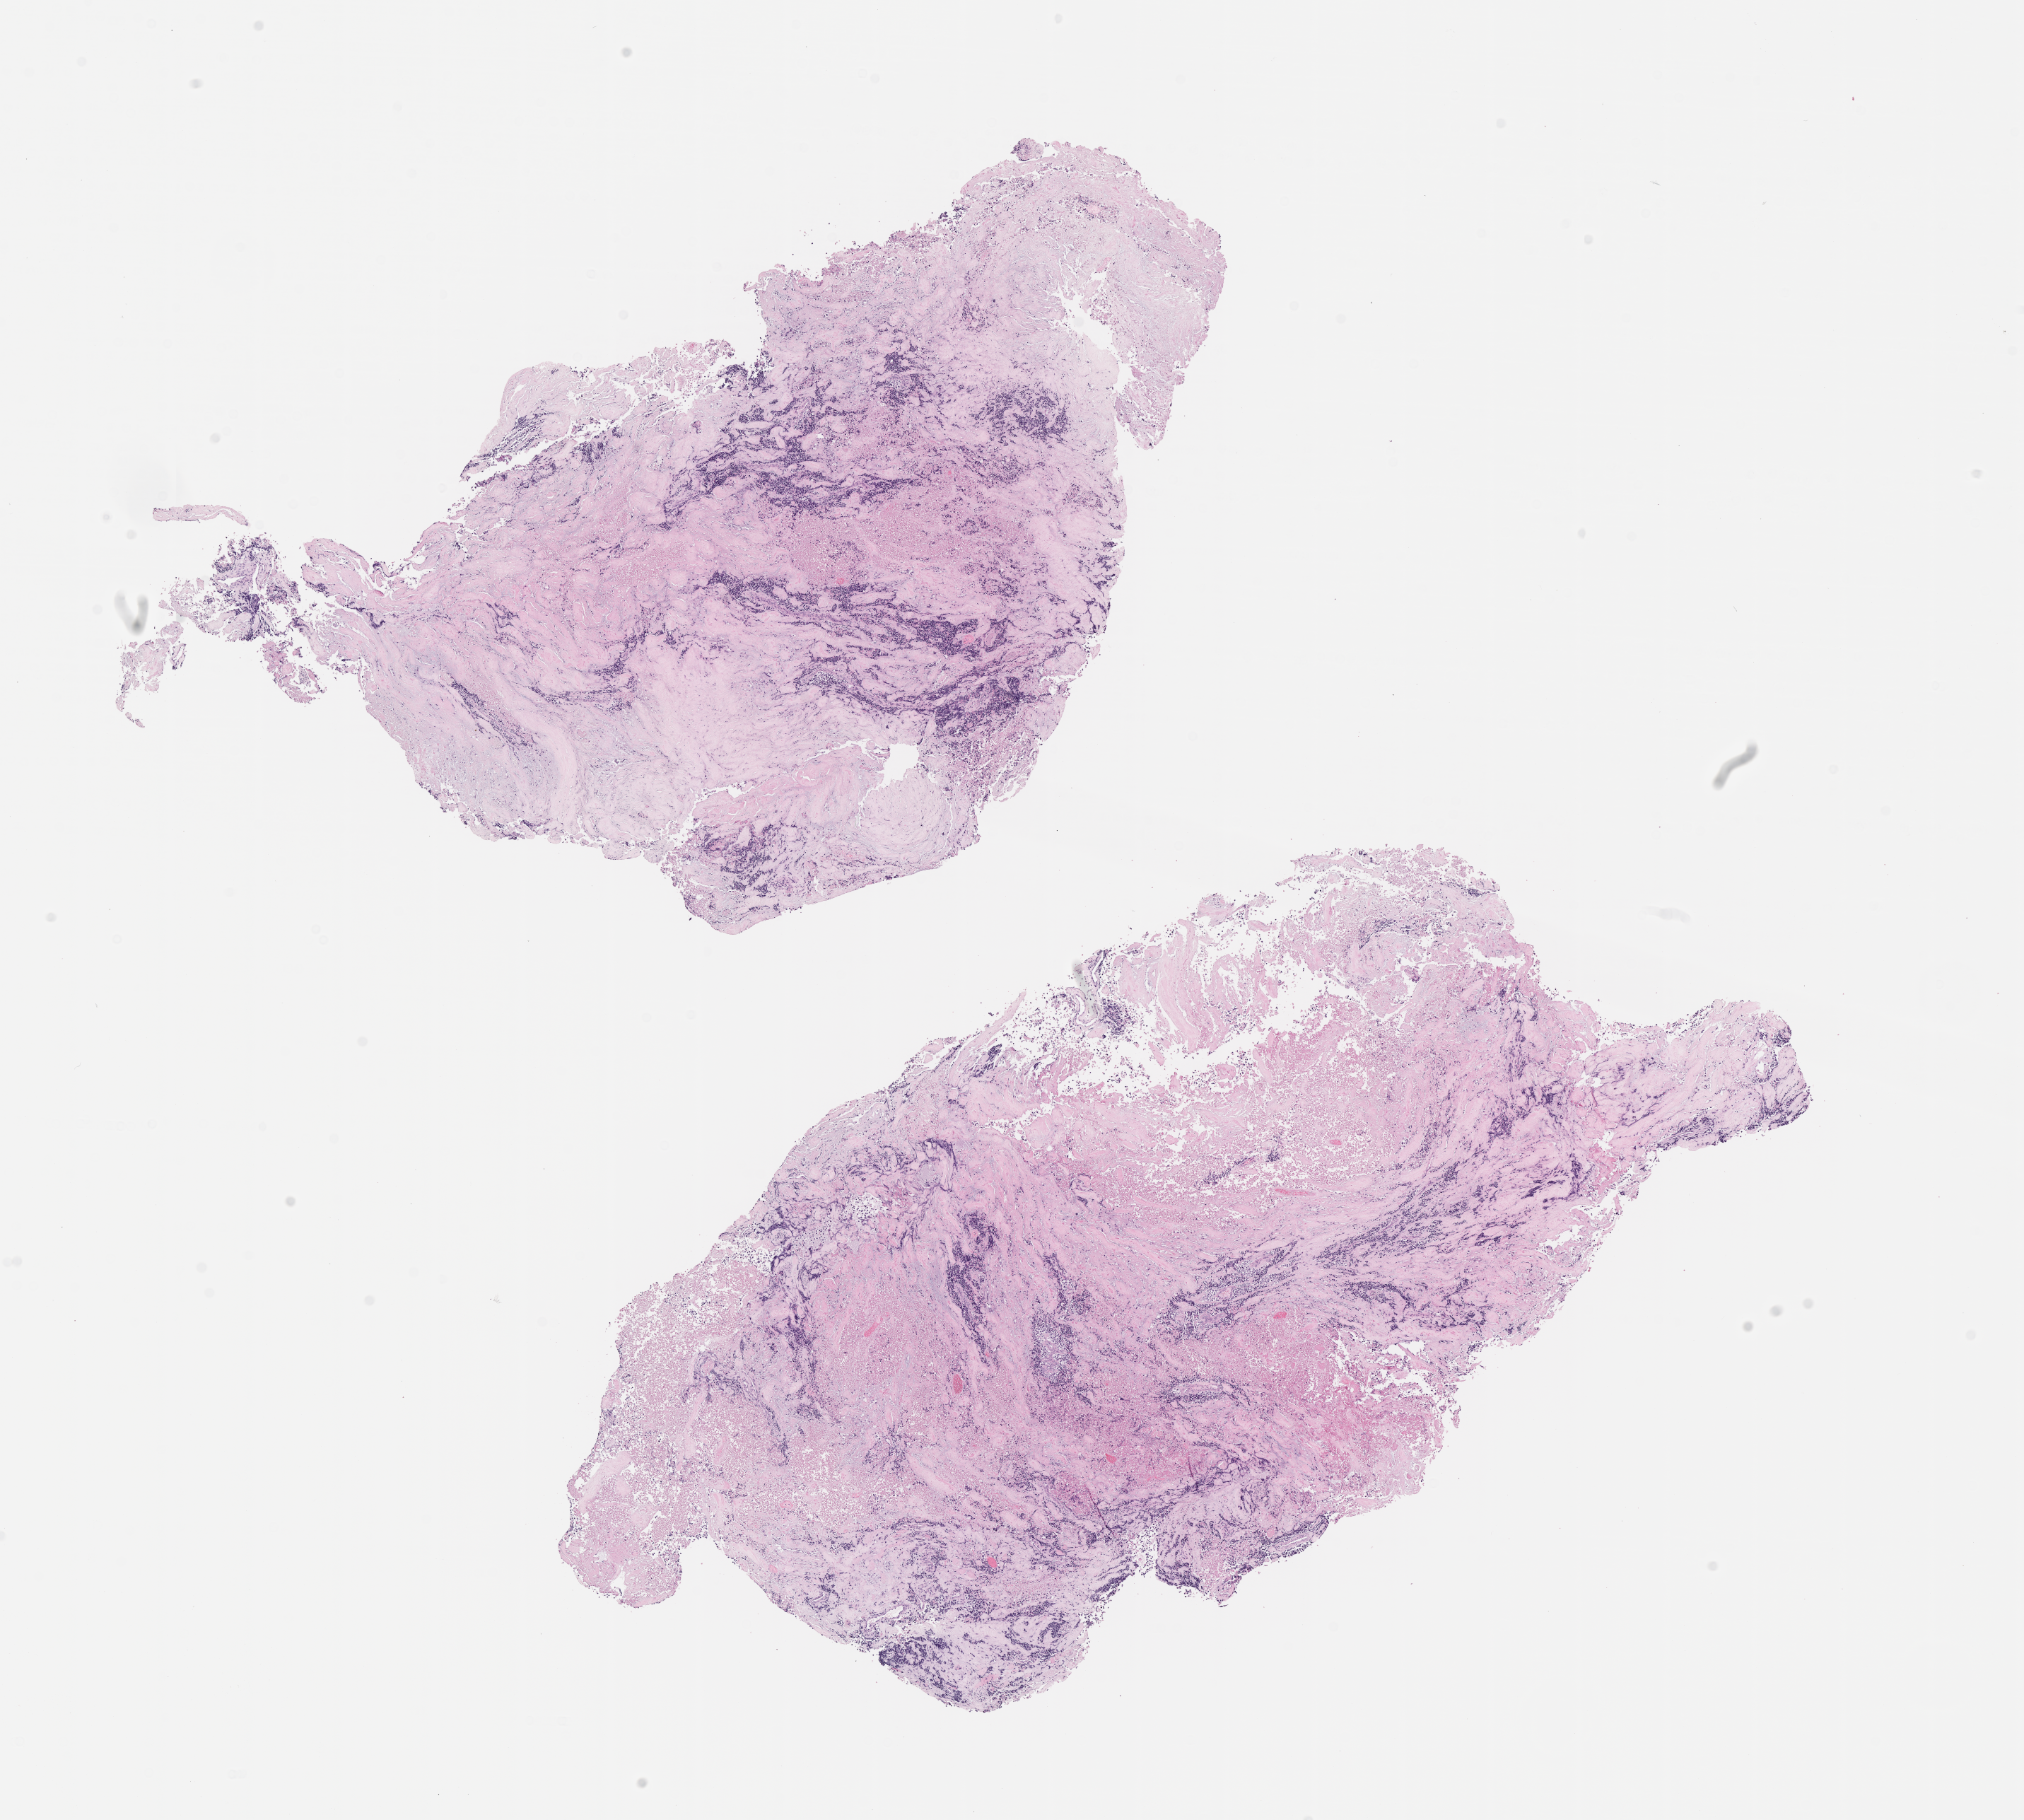
Digitized hematoxylin and eosin (H&E)-stained section of tumor tissue — shown as a low-resolution overview of the whole scanned area (about 11.6 x 10.4 mm); formalin-fixed, paraffin-embedded (FFPE) tissue; site: bone, tibia-left. Patient: female, age 16.4 years at diagnosis.
Diagnosis: rhabdomyosarcoma; histological classification: alveolar rhabdomyosarcoma.